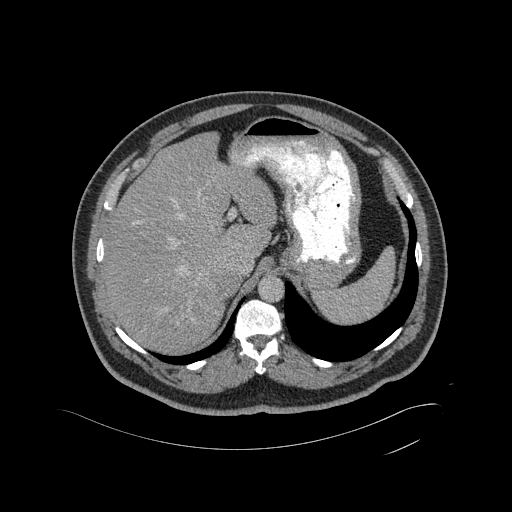
Contrast-enhanced abdominal CT, one axial slice; position 347 of 433 along the scan axis; soft-tissue window (W 400 / L 40 HU); 2 mm slice thickness; 512 × 512 image matrix, field of view 500 × 500 mm. Patient: male, 56 years. Case-level facts recorded for this patient, not image findings: diagnosis: adrenocortical carcinoma; tumour side: right adrenal; tumour size at pathology: 11.6 cm; Ki-67 index: 50 %; stage (as recorded): 3.
Outlined on this slice (semi-automatic segmentation, software-assisted and operator-edited):
- mass: bounding box <218,276,240,297> (left, top, right, bottom; pixels)